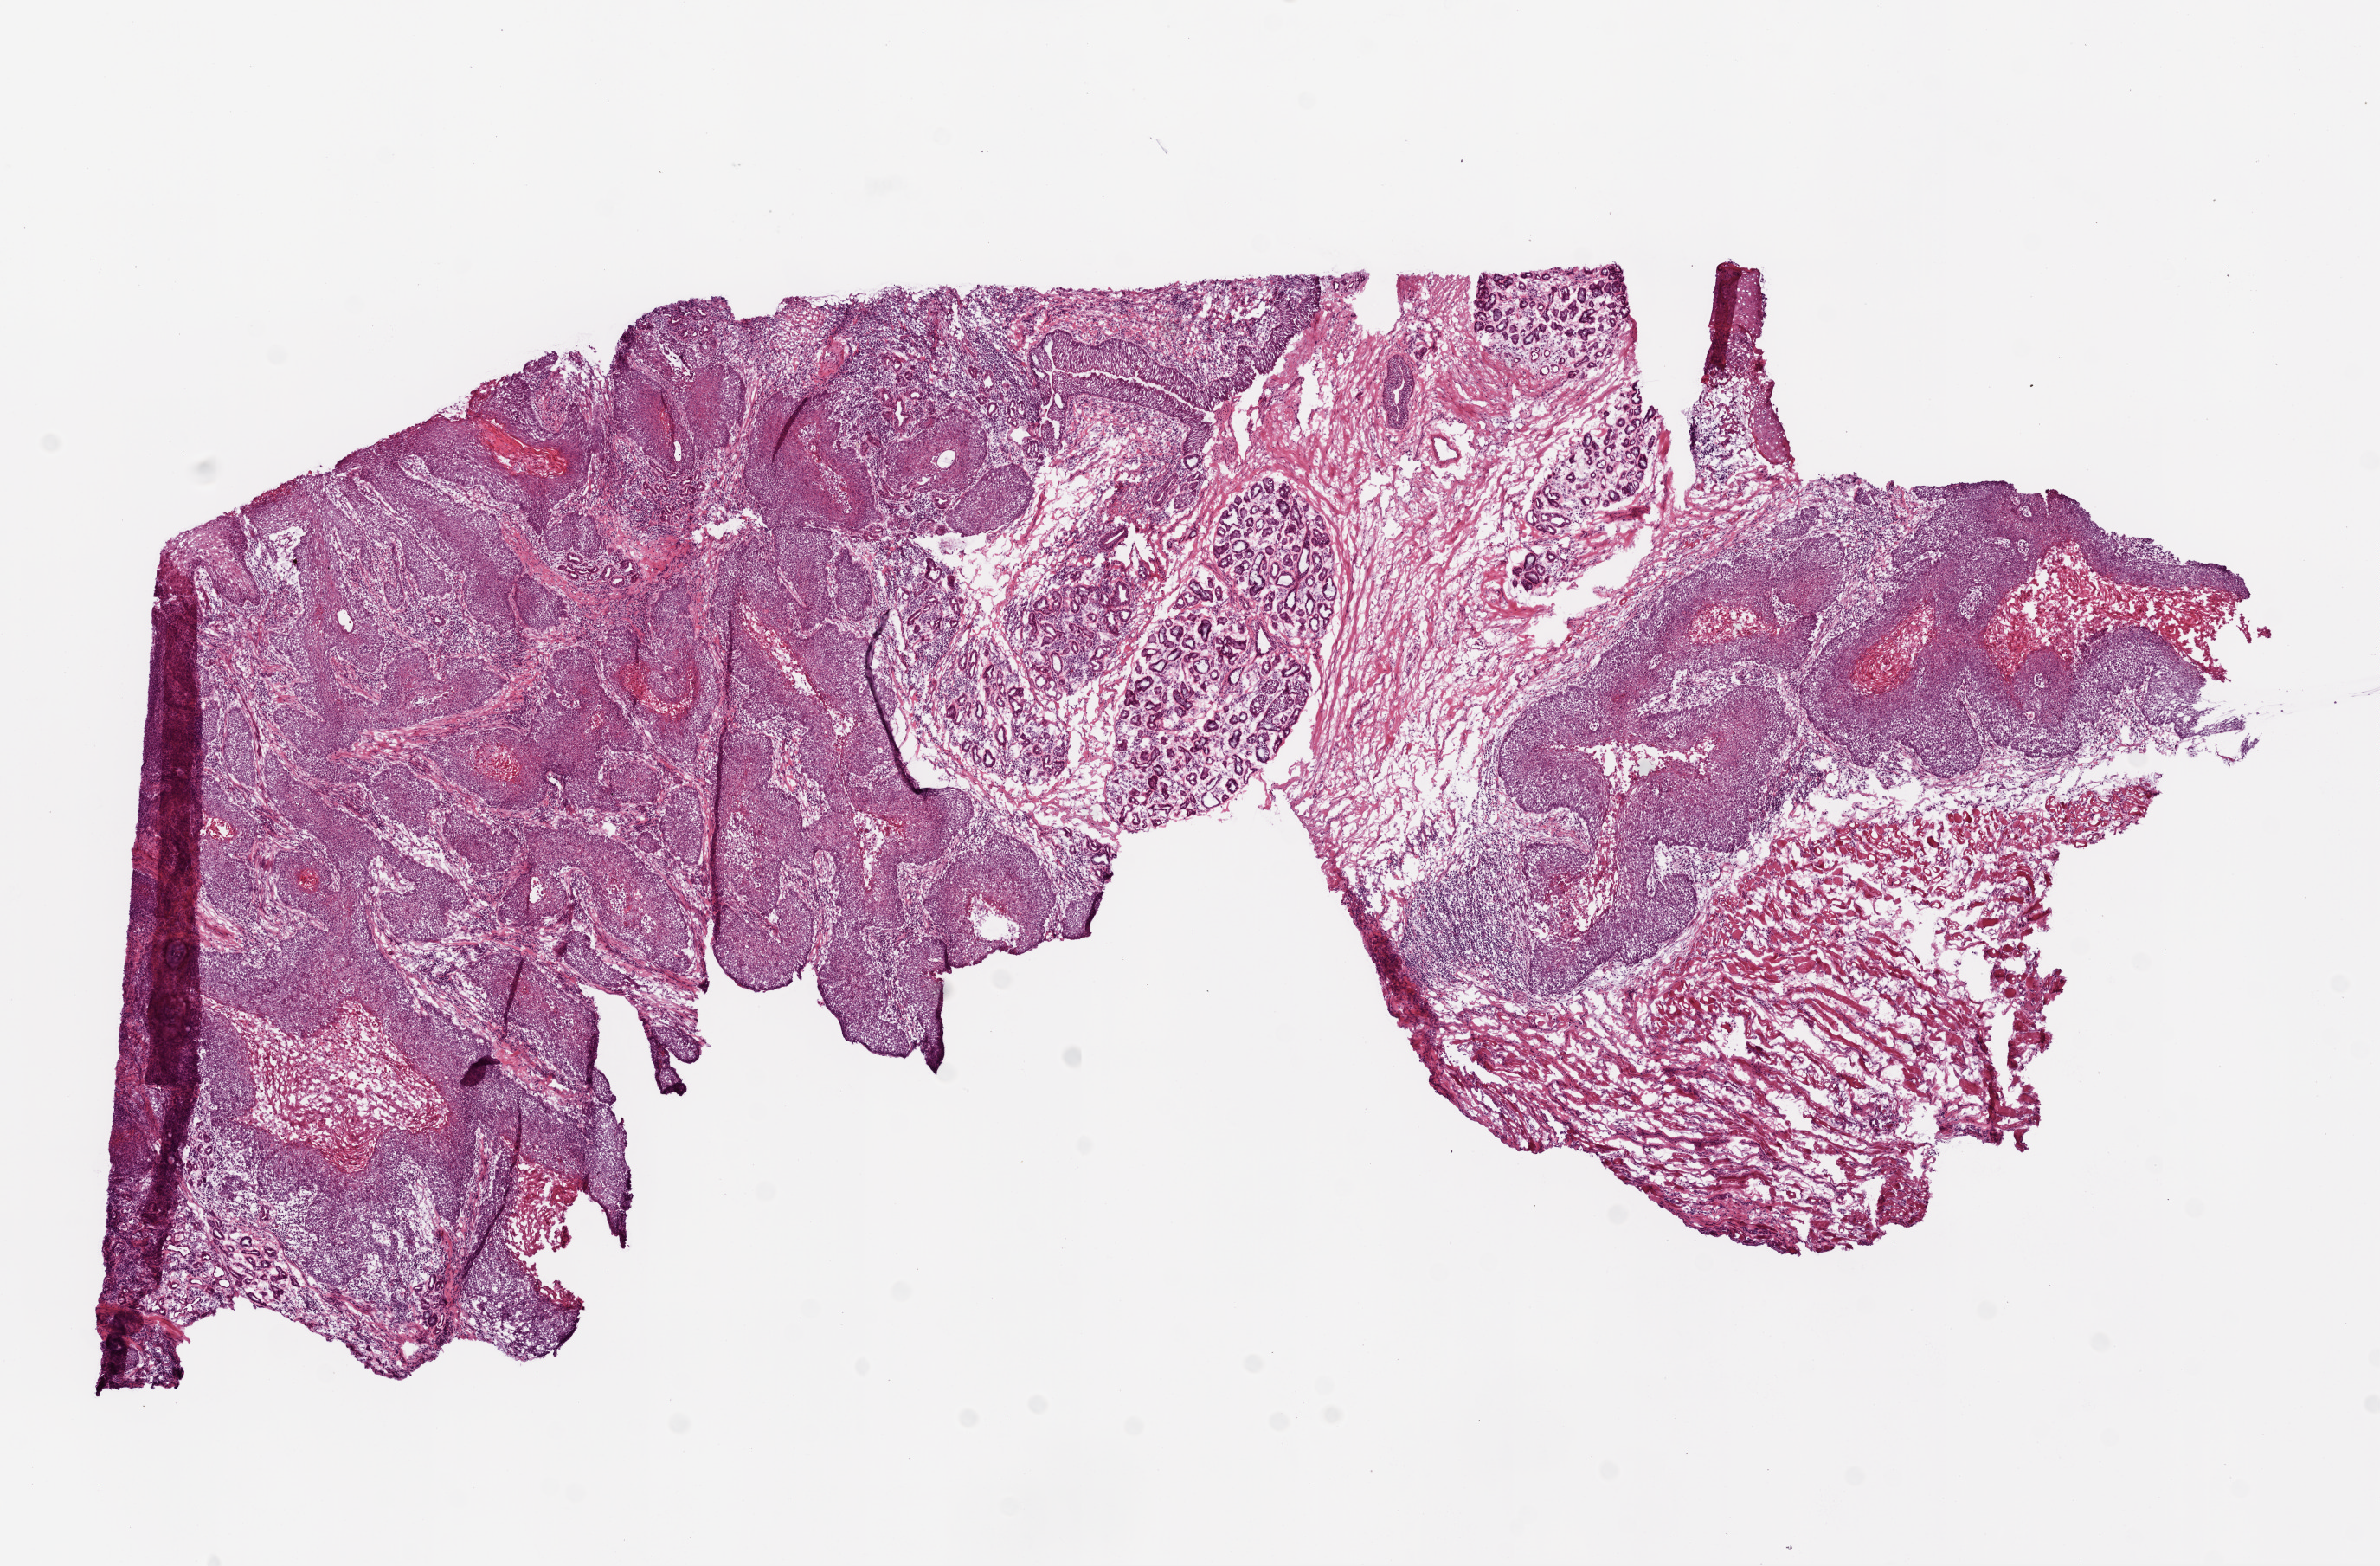
Whole-slide histology image, Hematoxylin and eosin (H&E) stained — whole scanned area (about 11.0 x 7.3 mm) shown as a low-resolution overview; frozen section from the top of the tissue portion; primary tumour sample from the head and neck. Male, age 68 years at initial diagnosis. Histologic grade: G2 (moderately differentiated). Slide review estimates, as recorded: tumour cells 65%, tumour nuclei 70%, normal cells 20%, stromal cells 15%, necrosis 0%.
Pathologic diagnosis: Squamous cell carcinoma, NOS. AJCC pathologic stage: IVA.